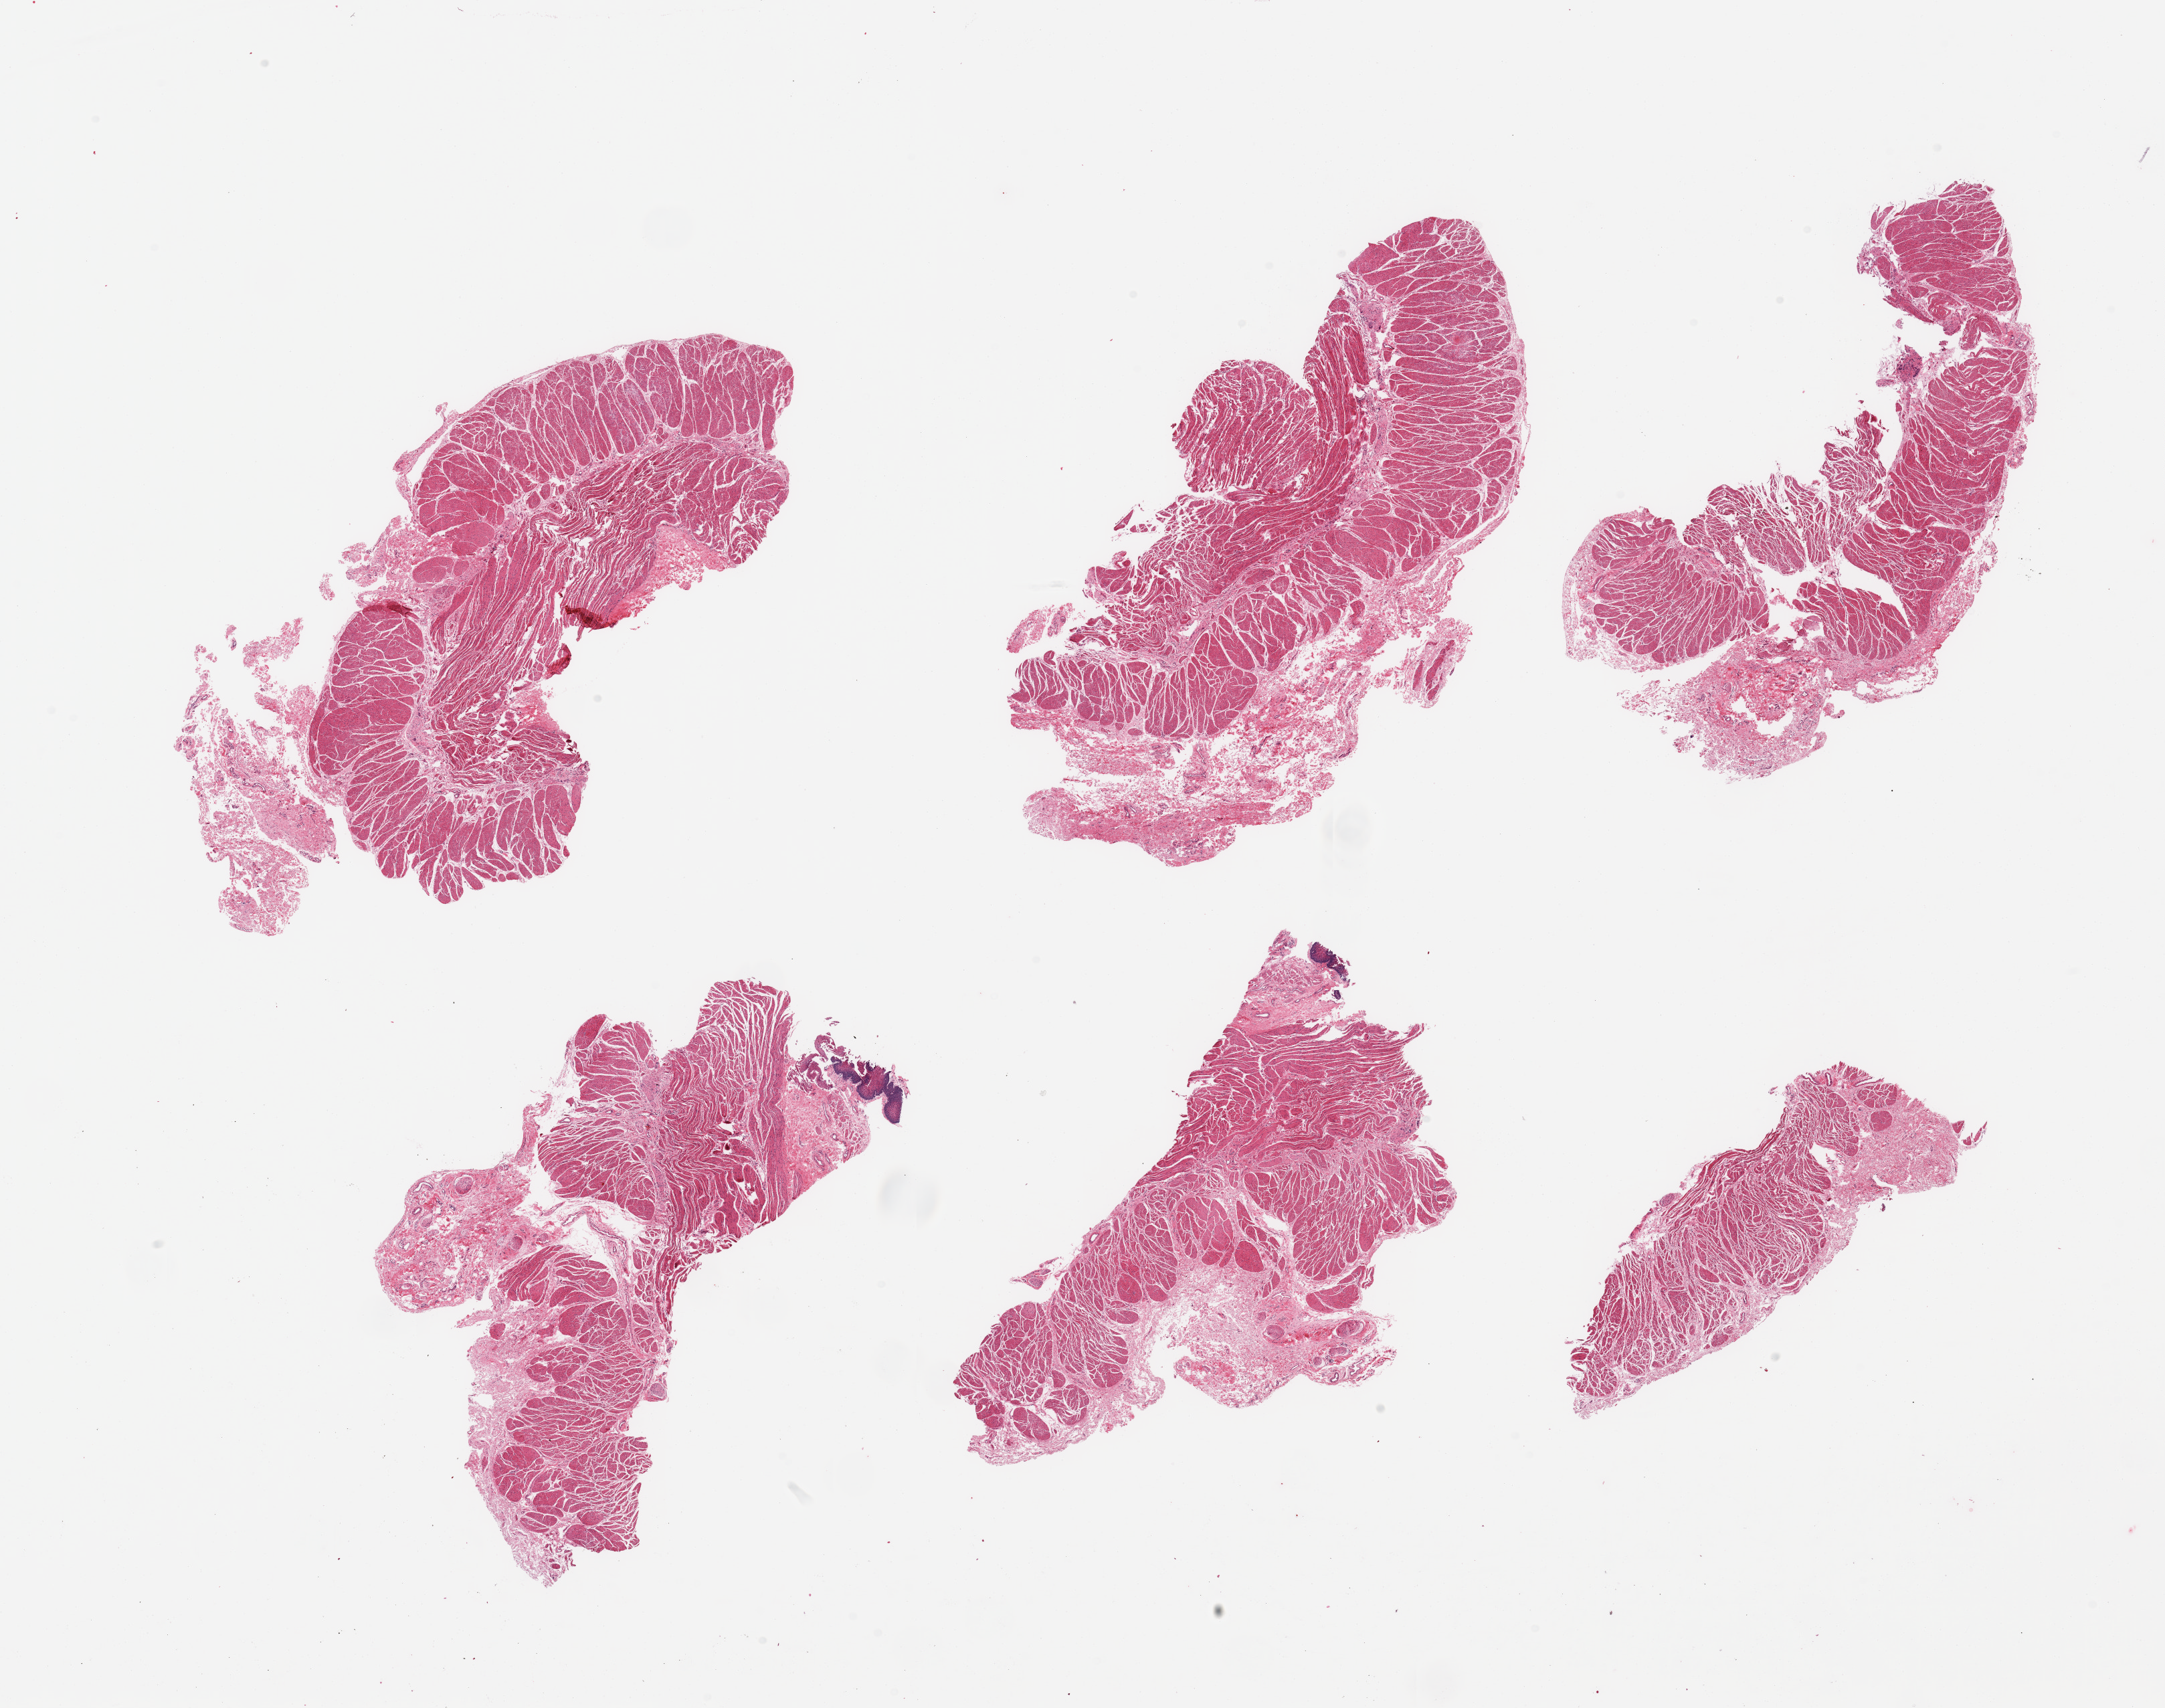
Digitized H&E-stained section, brightfield, a low-resolution overview of the entire scanned area, about 25.6 x 20.2 mm (slide scanned at 20x); PAXgene-fixed, paraffin-embedded tissue; section of esophageal muscle (target tissue); donor tissue sample.
Pathologist's review note for this sample: 6 pieces; target muscularis, two small fragments of residual mucosa.